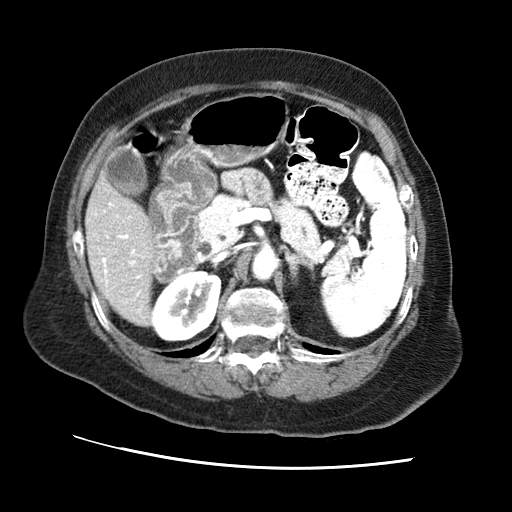
Contrast-enhanced abdominal CT (liver protocol), one axial slice. Position 27 of 65 along the scan axis. Reconstruction kernel STANDARD. 120 kVp. Soft-tissue window (W 400 / L 40 HU). 2.5 mm slice thickness. 512 × 512 image matrix. From the clinical record (not read from this slice): diagnosis: hepatocellular carcinoma (patient treated with transarterial chemoembolisation; whether this scan precedes or follows treatment is not stated here); TNM stage (as recorded): Stage-II; Child-Pugh class: A; tumour differentiation: no biopsy; tumour nodularity: multinodular.
Outlined on this slice (semi-automatic segmentation, software-assisted and operator-edited):
- liver parenchyma outside the tumour (the mass and vessels are separate outlines, so this box may not span the whole liver): bounding box <86,152,156,324> (left, top, right, bottom; pixels)
- liver vessels: <95,203,144,313>